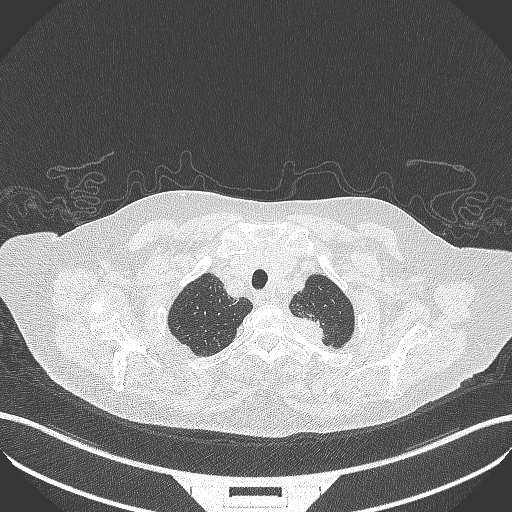
Chest CT, one axial slice. Position 309 of 353 along the scan axis. Reconstruction kernel B70f. 100 kVp. Lung window (W 1500 / L -600 HU). 1 mm slice thickness. 512 × 512 image matrix, field of view 400 × 400 mm. Female patient, age 81 years. From the clinical record (not read from this slice): clinical TNM (as recorded): T2a N0 M0.
Annotated regions visible in this slice (bounding box drawn by a radiologist):
- lung tumour (recorded histology: adenocarcinoma): box from (x=292, y=303) to (x=328, y=344) px